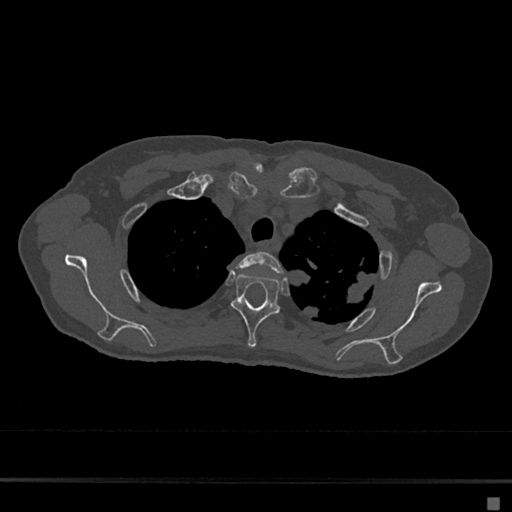
CT including the spine, one axial slice. Slice 541 of 797 in the series (ordered by position). Reconstruction kernel Br40s/3. 120 kVp. Bone window (W 1800 / L 400 HU). 512 × 512 image matrix, field of view 360 × 360 mm. Female patient, age 68 years. Case-level facts recorded for this patient, not image findings: primary cancer: renal.
Annotated regions visible in this slice (semi-automatically segmented with operator editing):
- T2 vertebra: box from (x=237, y=251) to (x=283, y=274) px
- T3 vertebra: (x=231, y=274)–(x=280, y=348)